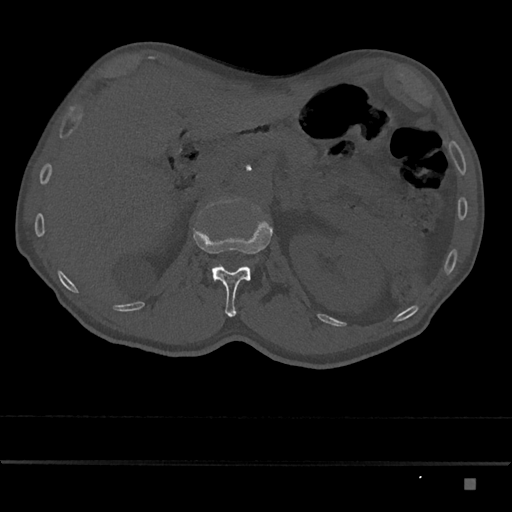
CT including the spine, one axial slice; slice 531 of 797 in the series (ordered by position); bone window (W 1800 / L 400 HU); 0.5 mm slice thickness; 512 × 512 image matrix, field of view 390 × 390 mm. Patient: male, 72 years. Case-level facts recorded for this patient, not image findings: primary cancer: prostate.
Annotated regions visible in this slice (semi-automatic segmentation, software-assisted and operator-edited):
- L1 vertebra: box from (x=193, y=221) to (x=273, y=317) px